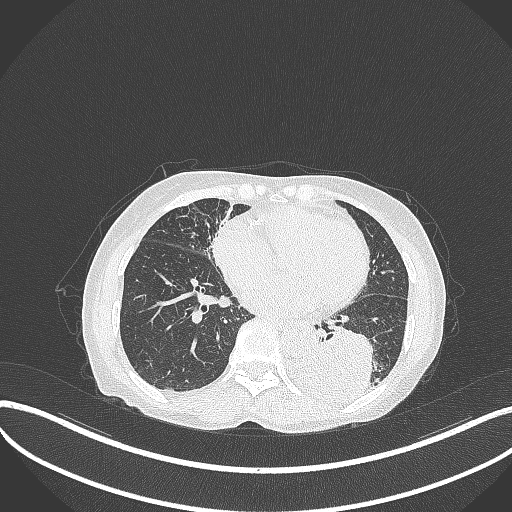
Chest CT, one axial slice. Slice 114 of 370 in the series (ordered by position). Reconstruction kernel B70f. 120 kVp. Lung window (W 1500 / L -600 HU). 512 × 512 image matrix. Female patient, age 78 years. From the clinical record (not read from this slice): clinical TNM (as recorded): T3 N0 M1.
Structures marked on this image (bounding box drawn by a radiologist):
- lung tumour (recorded histology: squamous cell carcinoma): bounding box (x1, y1, x2, y2) in pixels: (281, 322, 376, 409)